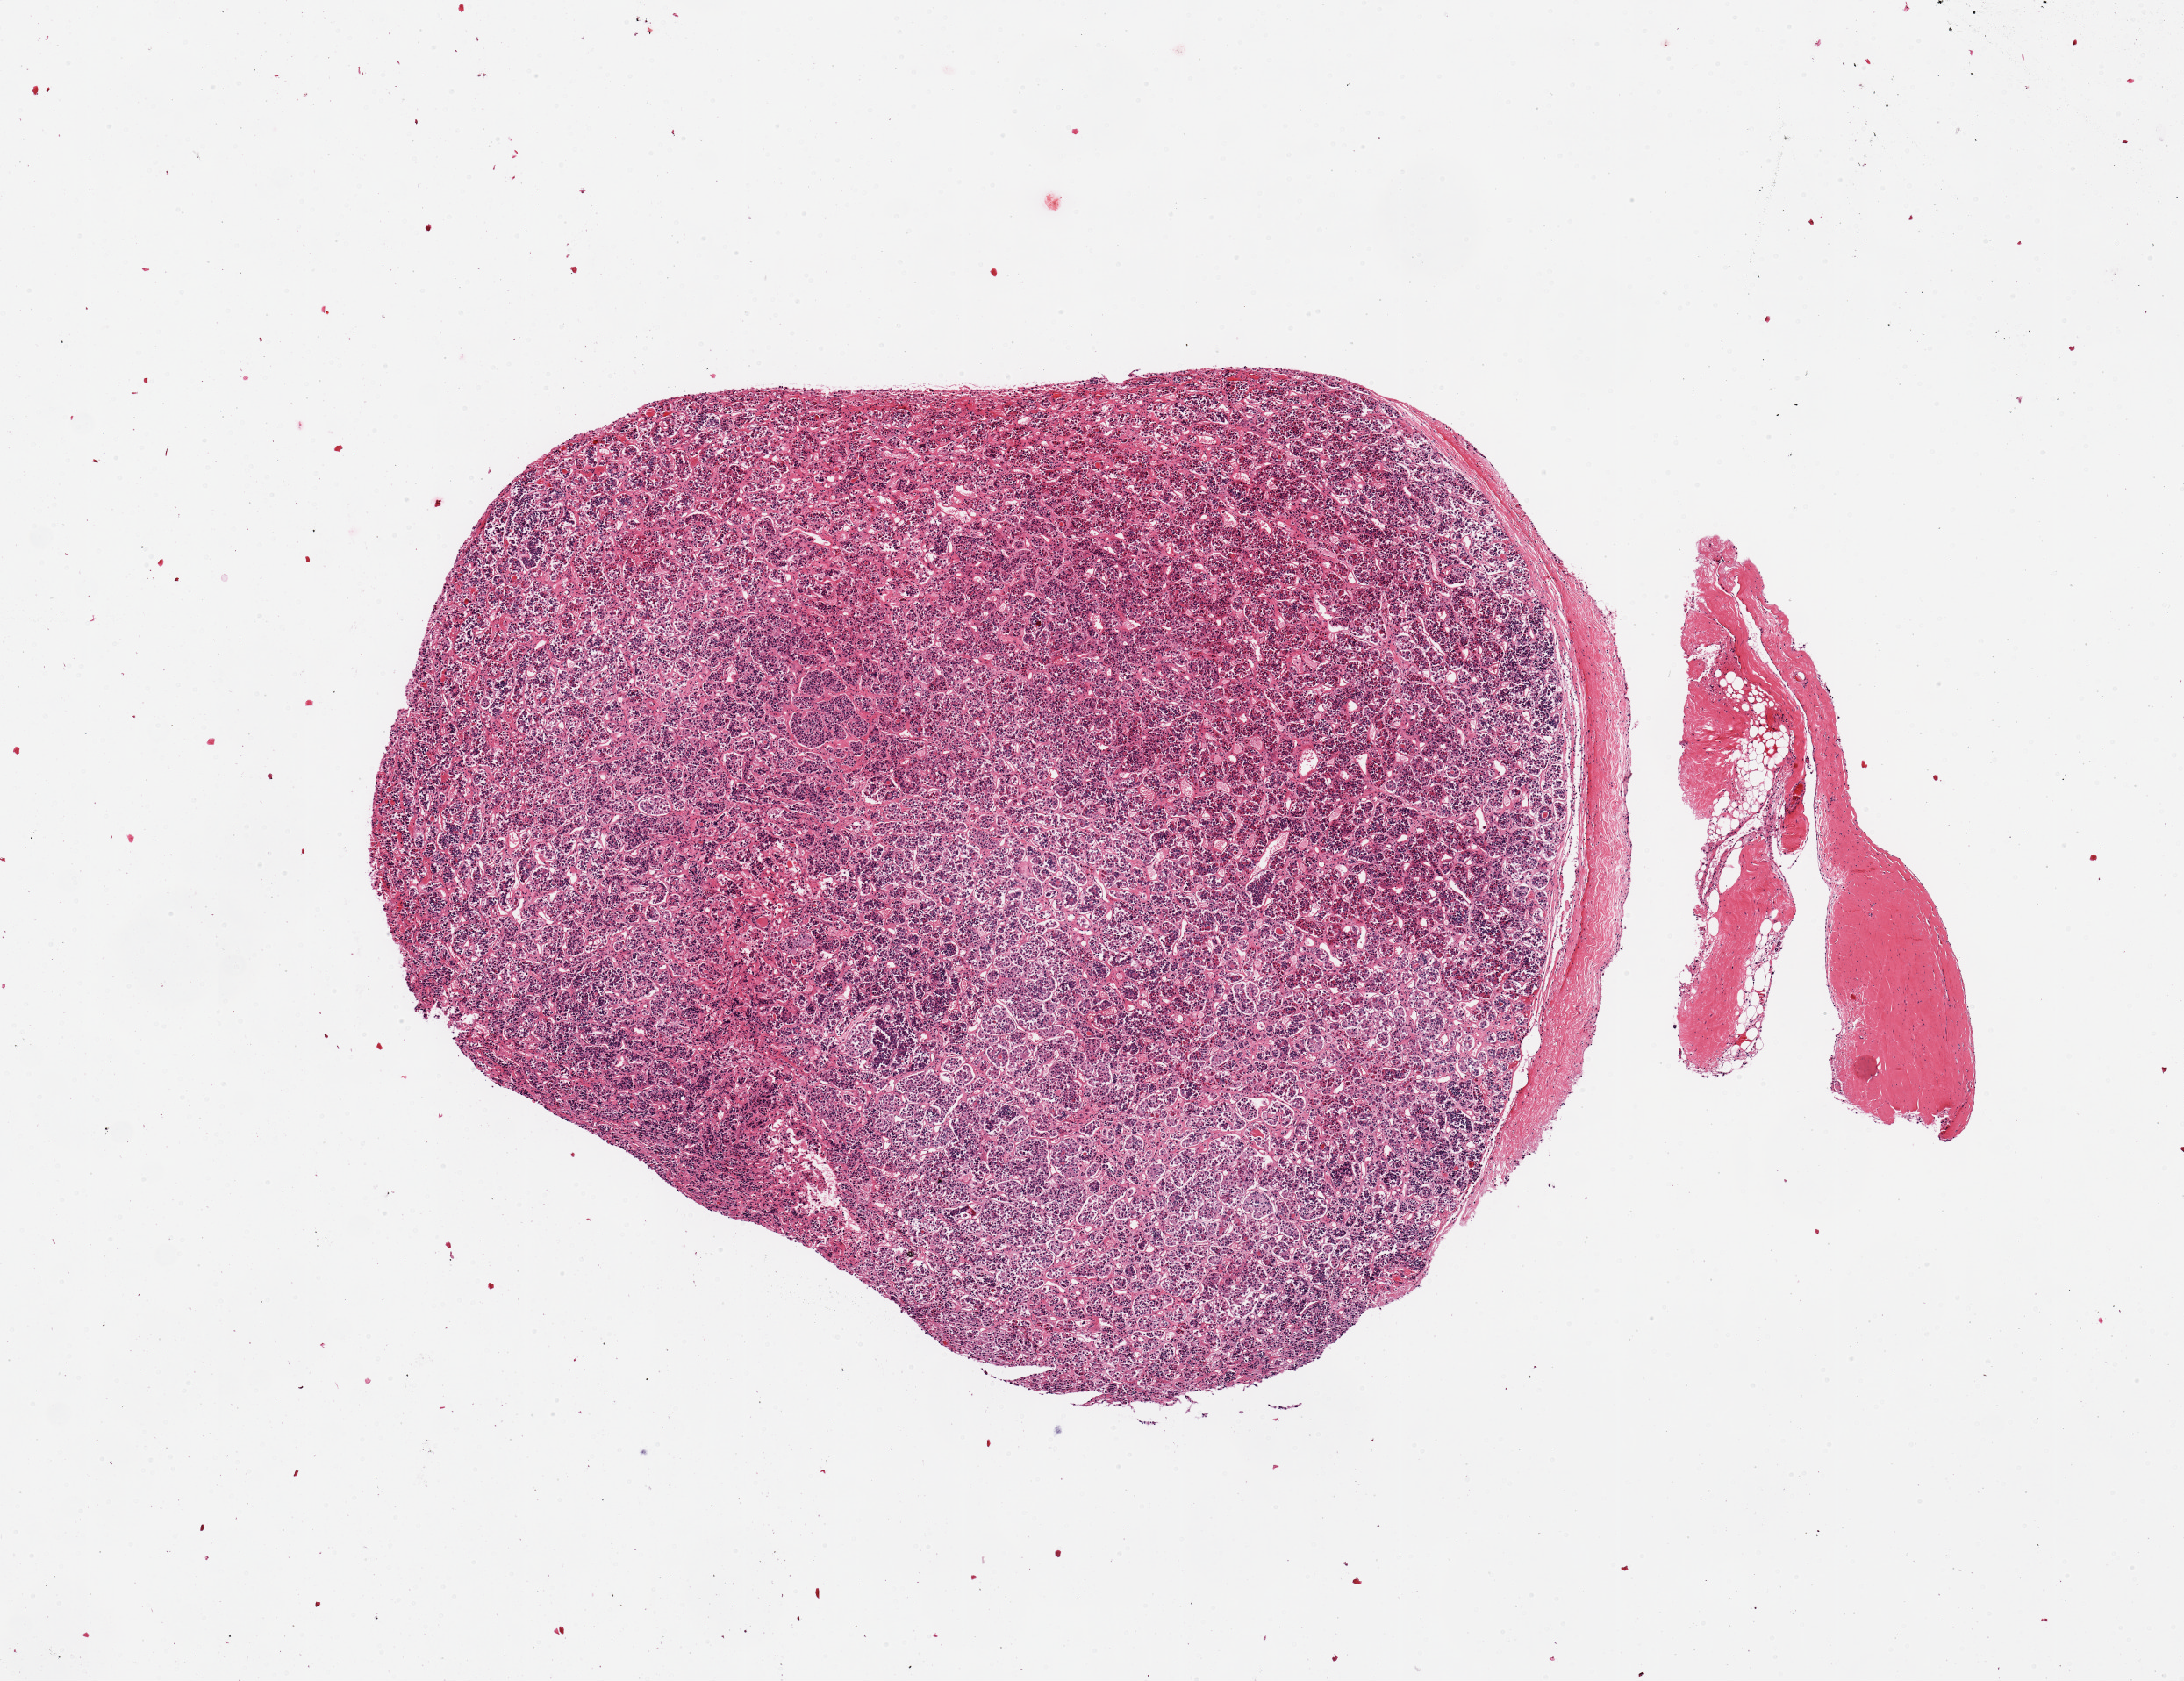
Digitized hematoxylin and eosin (H&E)-stained section, whole scanned area (about 9.8 x 7.6 mm, from a 20x scan) shown as a low-resolution overview, PAXgene-fixed paraffin-embedded (PFPE) section, sampled site (target tissue): pituitary, donor tissue sample. Donor: male.
• pathologist's review note for this sample: 1 piece, anterior